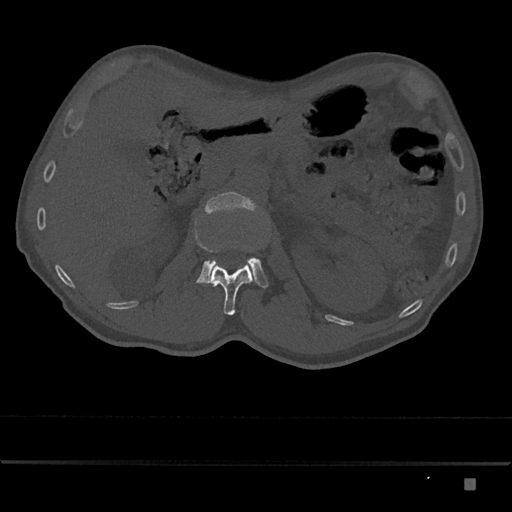
CT including the spine, one axial slice; reconstruction kernel Br40s/3; 120 kVp; bone window (W 1800 / L 400 HU); 0.5 mm slice thickness; 512 × 512 image matrix, field of view 390 × 390 mm. Patient: male, 72 years. From the clinical record (not read from this slice): primary cancer: prostate.
Structures marked on this image (semi-automatic segmentation, software-assisted and operator-edited):
- L1 vertebra: bounding box [x1, y1, x2, y2] px = [208, 259, 253, 315]
- L2 vertebra: [196, 191, 268, 288]